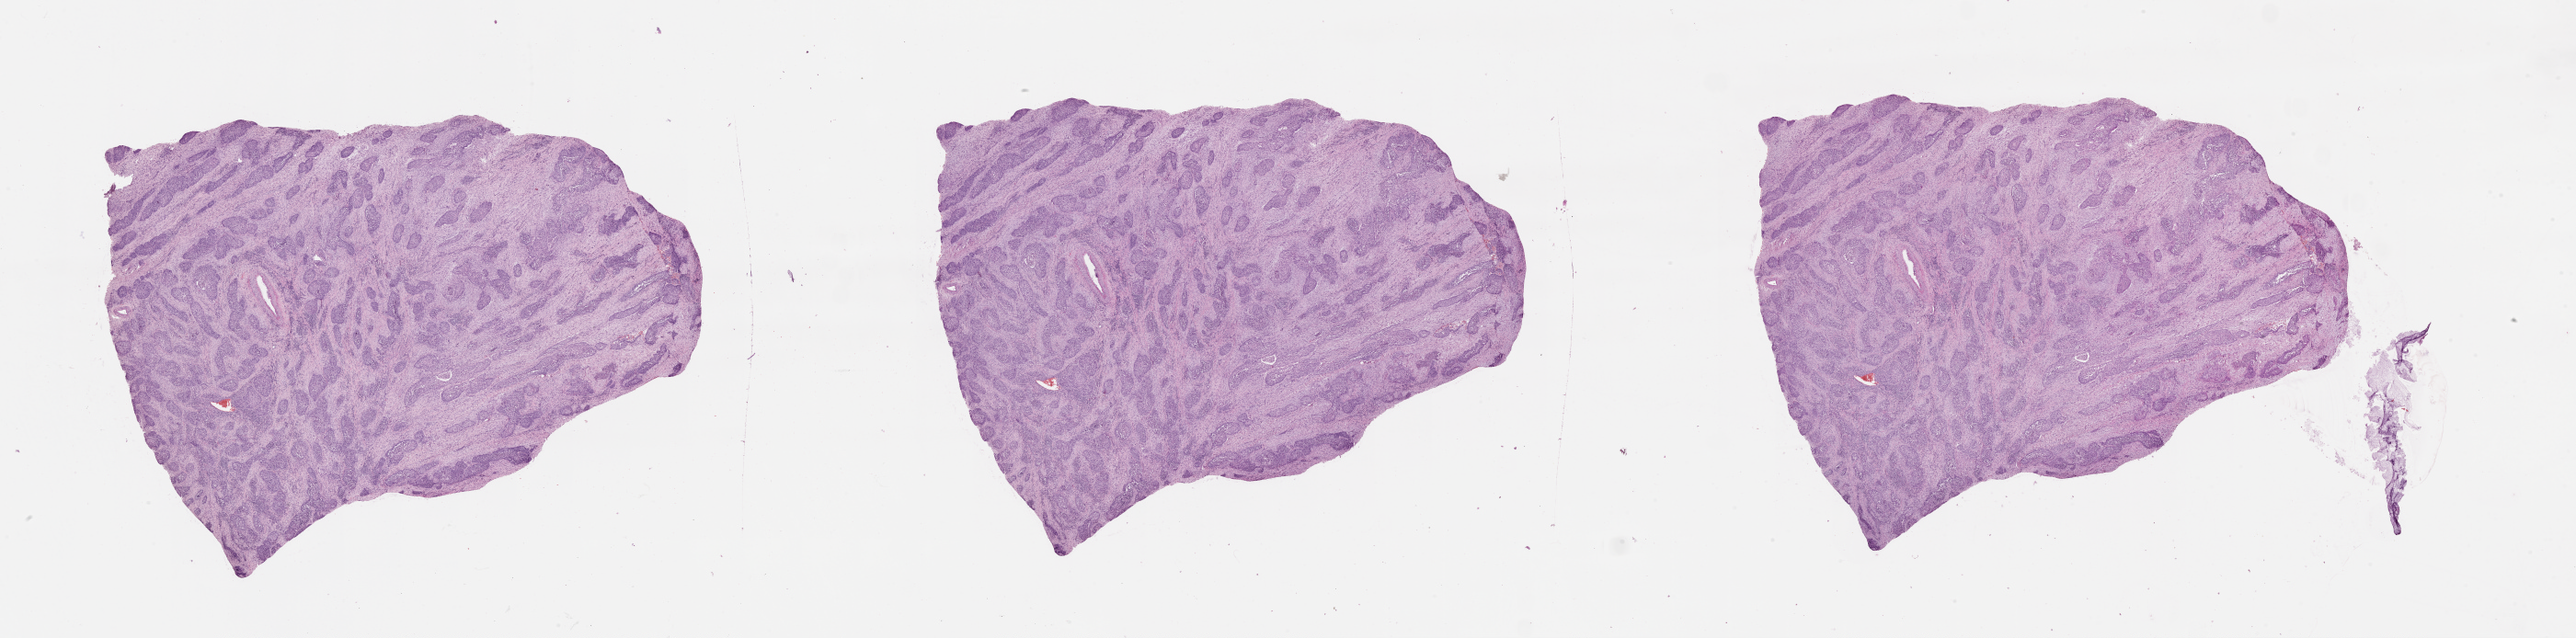
Digitized Hematoxylin and eosin (H&E) stained tissue section (whole slide), whole scanned area (about 45.1 x 11.2 mm, from a 20x scan) shown as a low-resolution overview. Lung, tumour tissue. Patient: male, age 74 years.
Patient diagnosis (cohort enrolment): squamous cell carcinoma (lung).